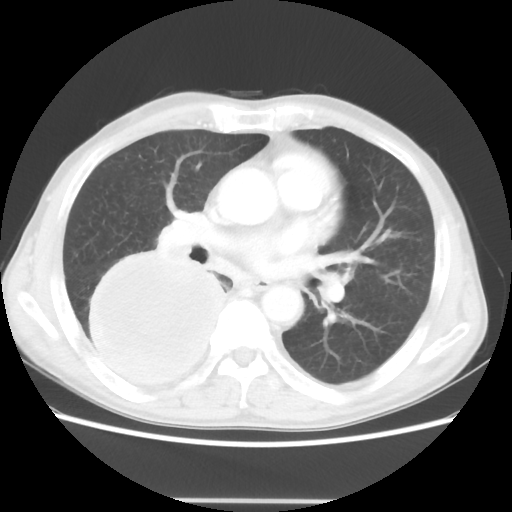
Chest CT, one axial slice; reconstruction kernel STANDARD; lung window (W 1500 / L -600 HU); 5 mm slice thickness; 512 × 512 image matrix, field of view 361 × 361 mm. Patient: male, 66 years. Case-level facts recorded for this patient, not image findings: clinical TNM (as recorded): T4 N1 M1; histopathological grade: G3.
Structures marked on this image (rectangle marked by the reading radiologist):
- lung tumour (recorded histology: small cell carcinoma): bounding box [x1, y1, x2, y2] px = [78, 249, 231, 395]